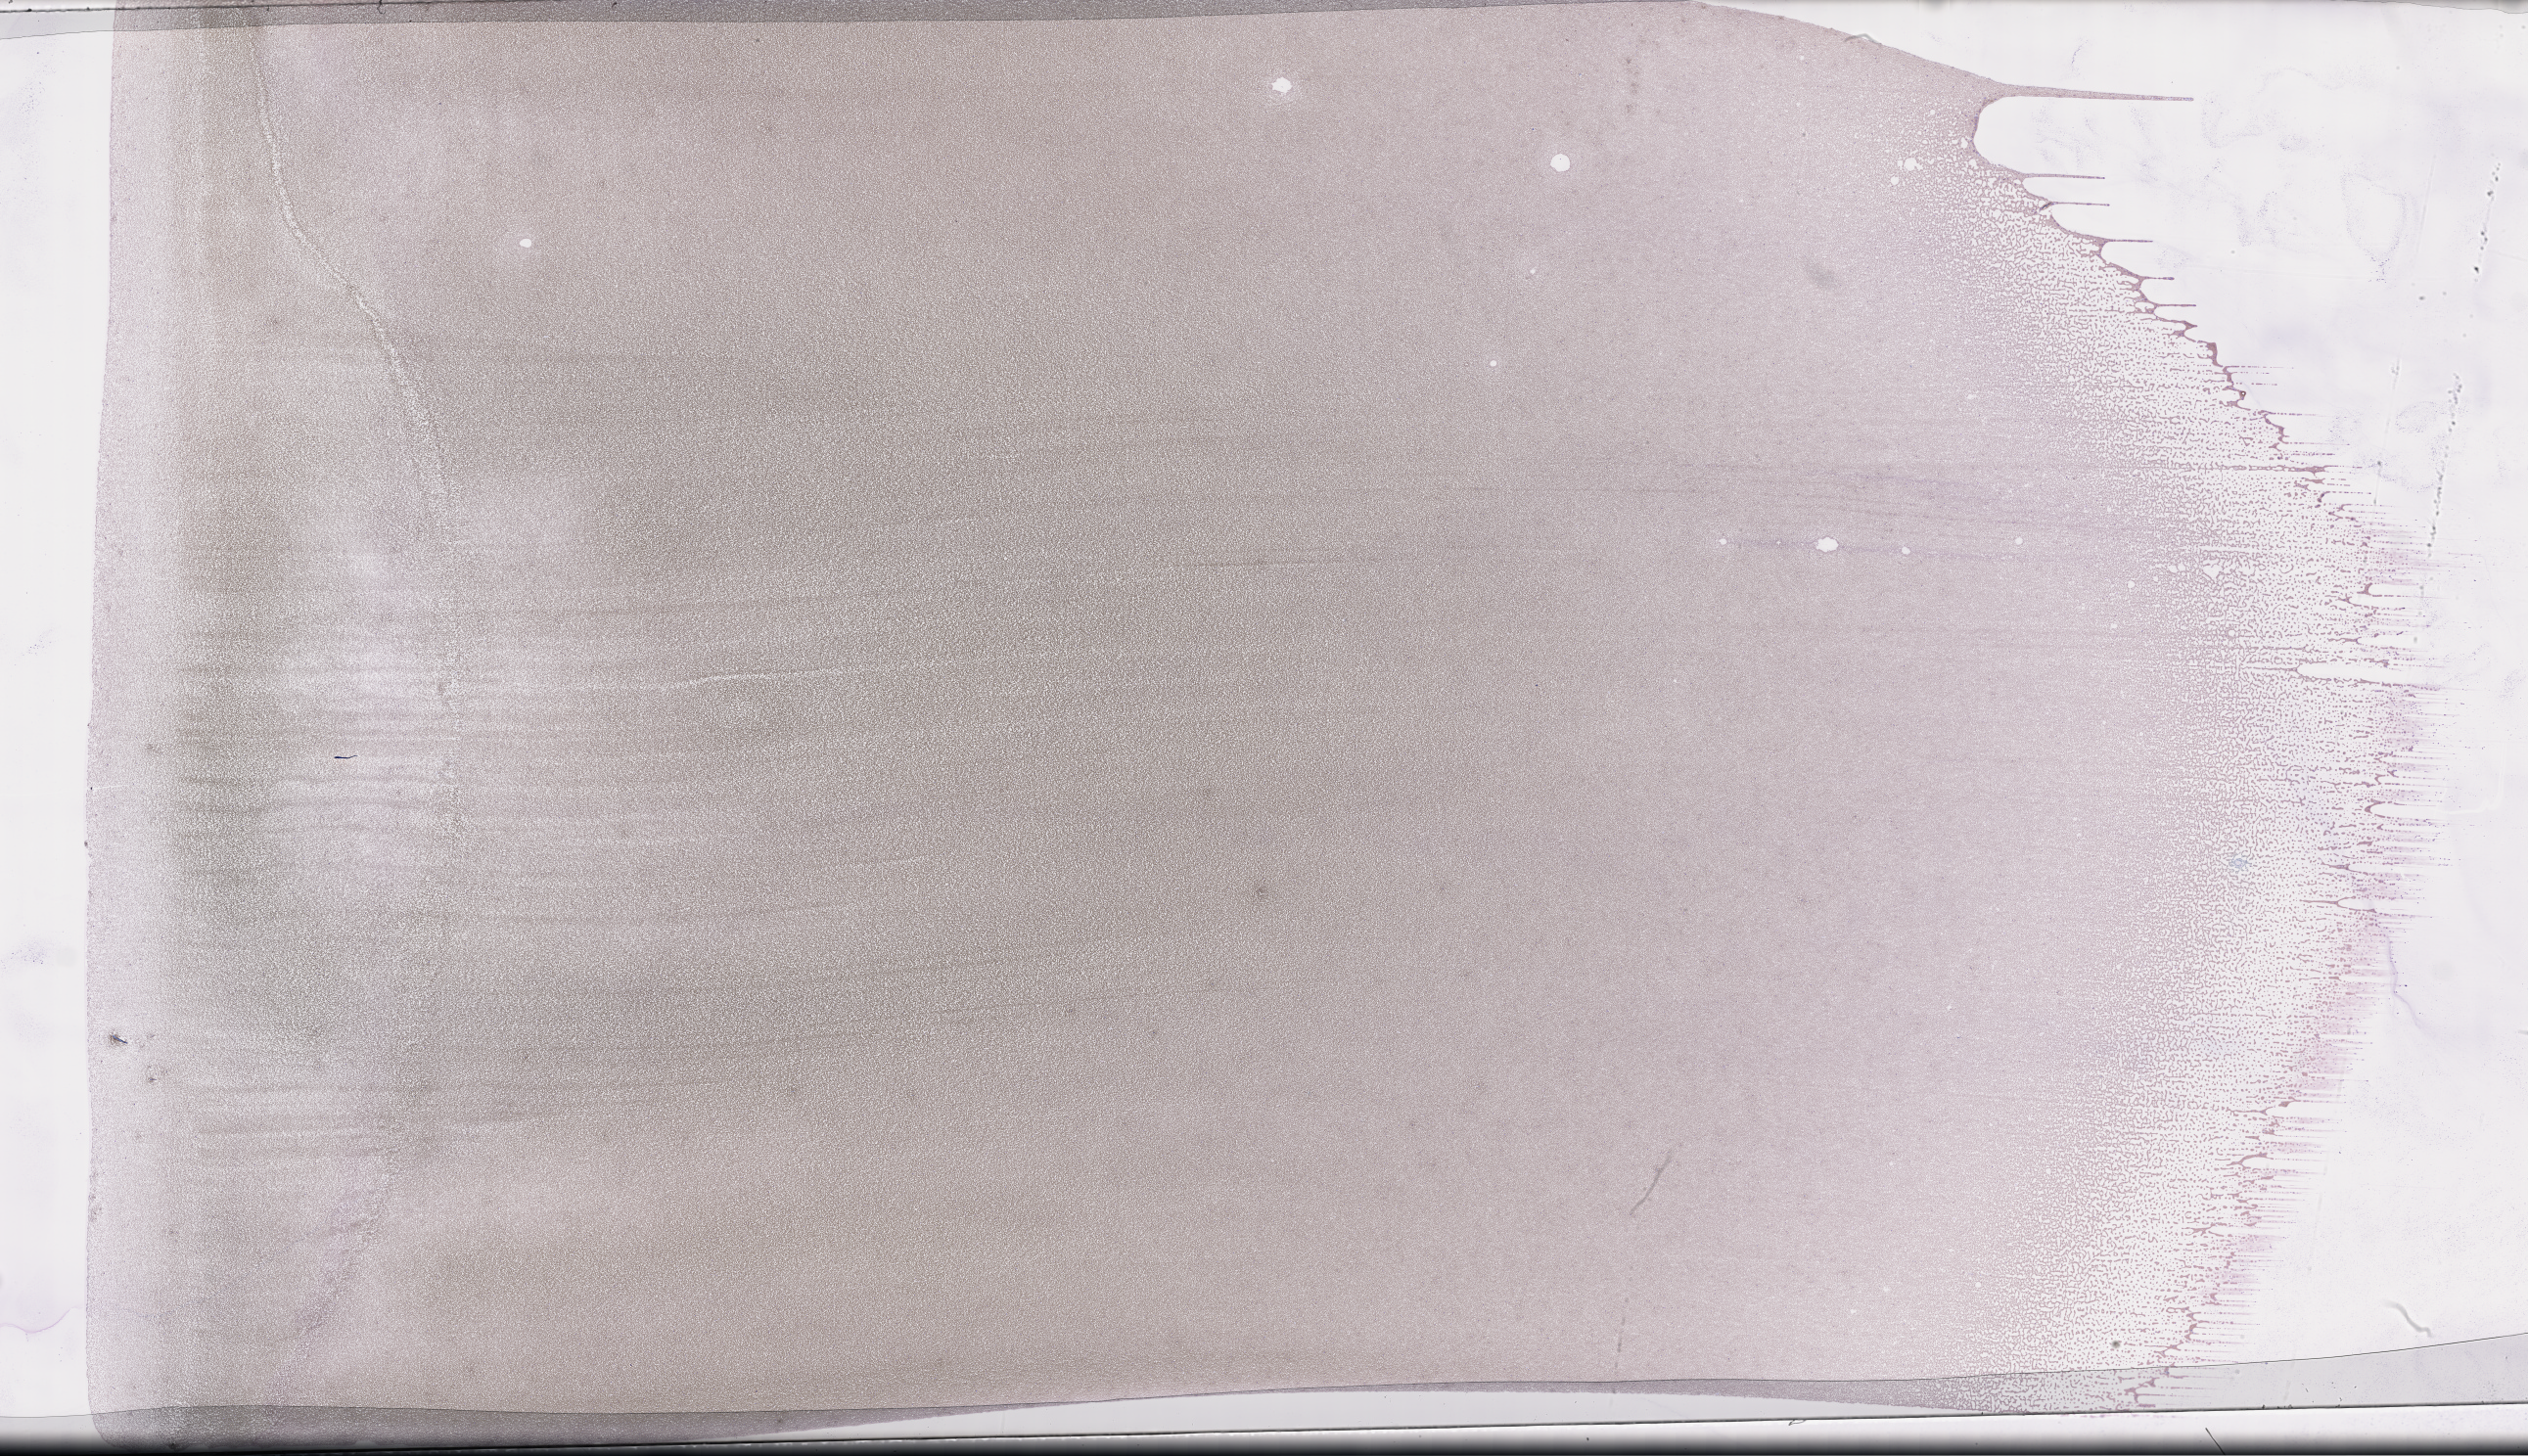
Wright-Giemsa-stained whole blood smear, whole-slide image, whole scanned area (about 41.7 x 24.0 mm) shown as a low-resolution overview; EDTA-anticoagulated smear; specimen time point: collected at baseline (before treatment). Patient: male.
- patient diagnosis: Plasma Cell Myeloma